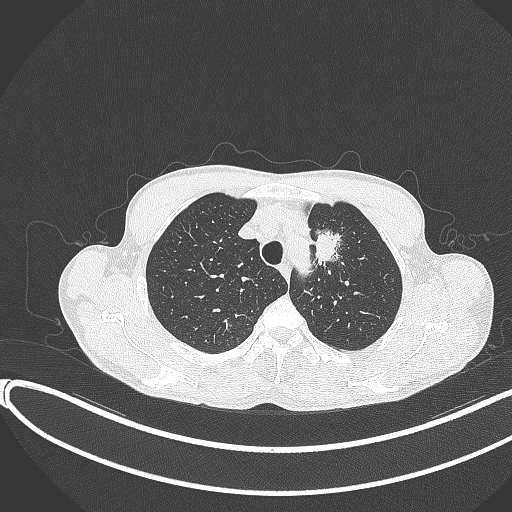
Chest CT, one axial slice. Reconstruction kernel B70f. 120 kVp. Lung window (W 1500 / L -600 HU). 1 mm slice thickness. 512 × 512 image matrix, field of view 400 × 400 mm. Patient: male, 58 years. From the clinical record (not read from this slice): clinical TNM (as recorded): T1c N1 M0.
Outlined on this slice (rectangle marked by the reading radiologist):
- lung tumour (recorded histology: adenocarcinoma): bounding box (x1, y1, x2, y2) in pixels: (311, 226, 346, 268)